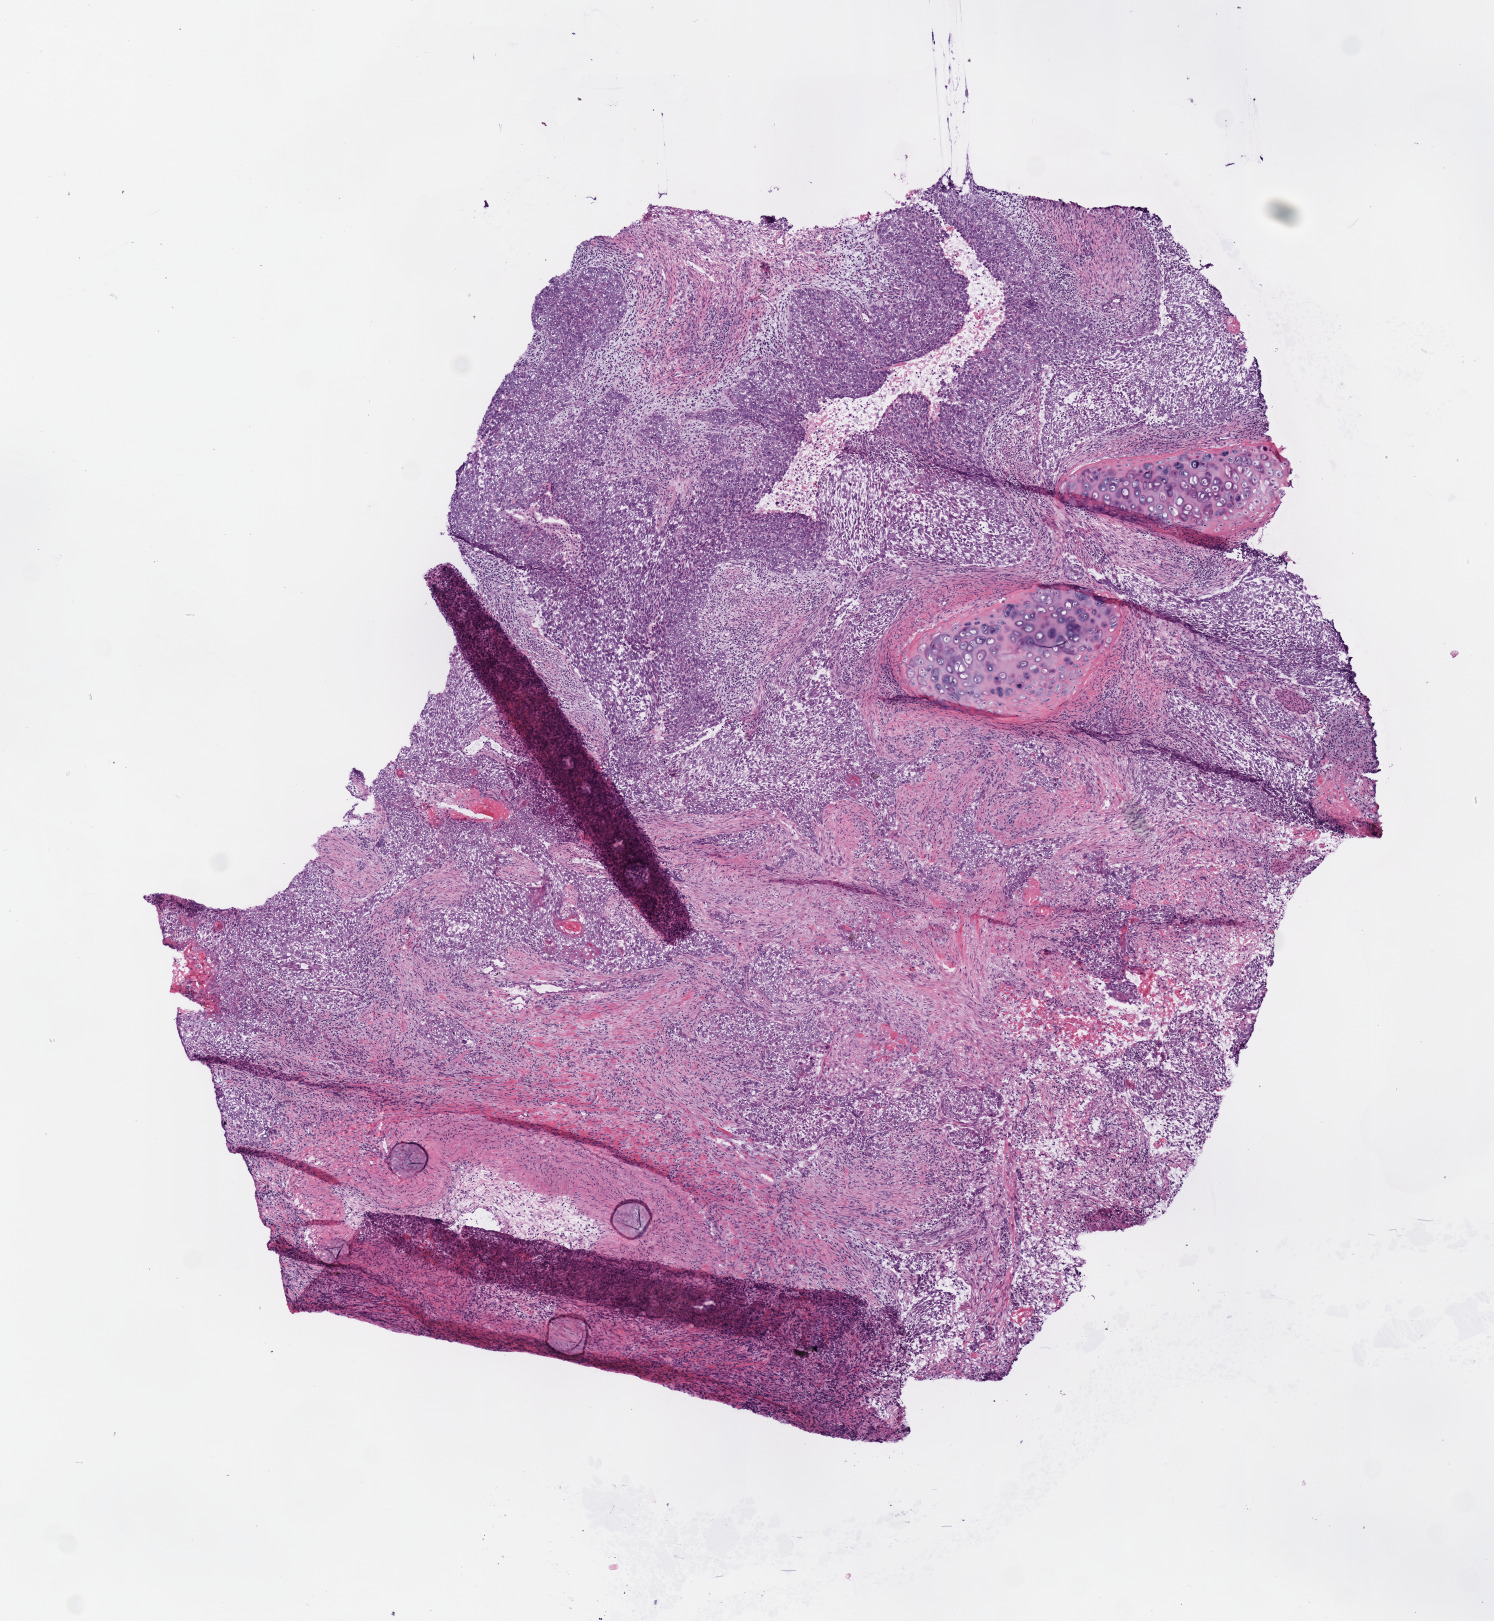
Digitized H&E-stained tissue section (whole slide), low-resolution overview of the scanned area, about 5.9 x 6.4 mm (slide scanned at 40x). Frozen section. Lung, primary tumour sample. Male, age 56 years at initial diagnosis. Slide review estimates, as recorded: tumour cells 70%, tumour nuclei 57%, normal cells 0%, stromal cells 30%, necrosis 0%. Inflammatory infiltration, as recorded: lymphocyte infiltration 35%, monocyte infiltration 0%, neutrophil infiltration 2%.
AJCC pathologic stage: IIB (7th edition). Diagnosis: Squamous cell carcinoma, NOS (upper lobe, lung).